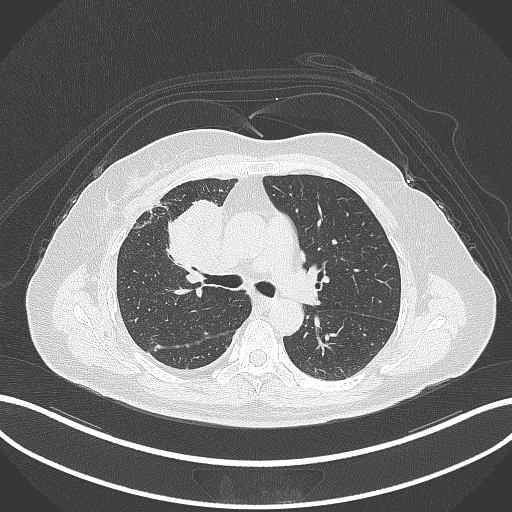
Chest CT, one axial slice. Position 175 of 305 along the scan axis. Reconstruction kernel B70f. 120 kVp. Lung window (W 1500 / L -600 HU). 1 mm slice thickness. 512 × 512 image matrix, field of view 400 × 400 mm. Female patient, age 52 years. Case-level facts recorded for this patient, not image findings: clinical TNM (as recorded): T3 N1 M1.
Annotated regions visible in this slice (rectangle marked by the reading radiologist):
- lung tumour (recorded histology: adenocarcinoma): box from (x=161, y=196) to (x=226, y=284) px